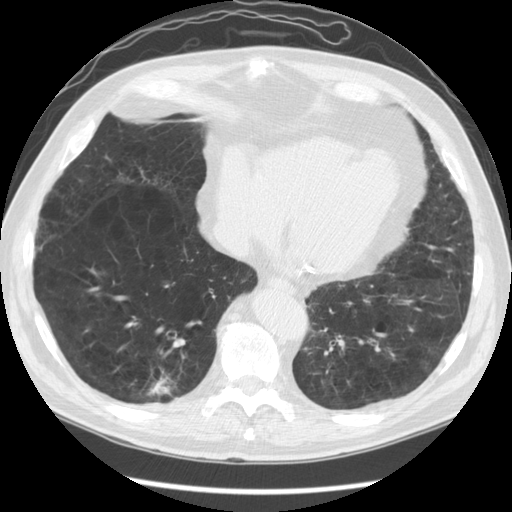
Low-dose screening chest CT, one axial slice; slice 45 of 141 in the series (ordered by position); reconstruction kernel STANDARD; lung window (W 1500 / L -600 HU); 2.5 mm slice thickness; 512 × 512 image matrix.
Outlined on this slice (expert manual segmentation):
- lesion 1 (tumor, lower lobe of right lung): bounding box (x1, y1, x2, y2) in pixels: (147, 377, 173, 396)